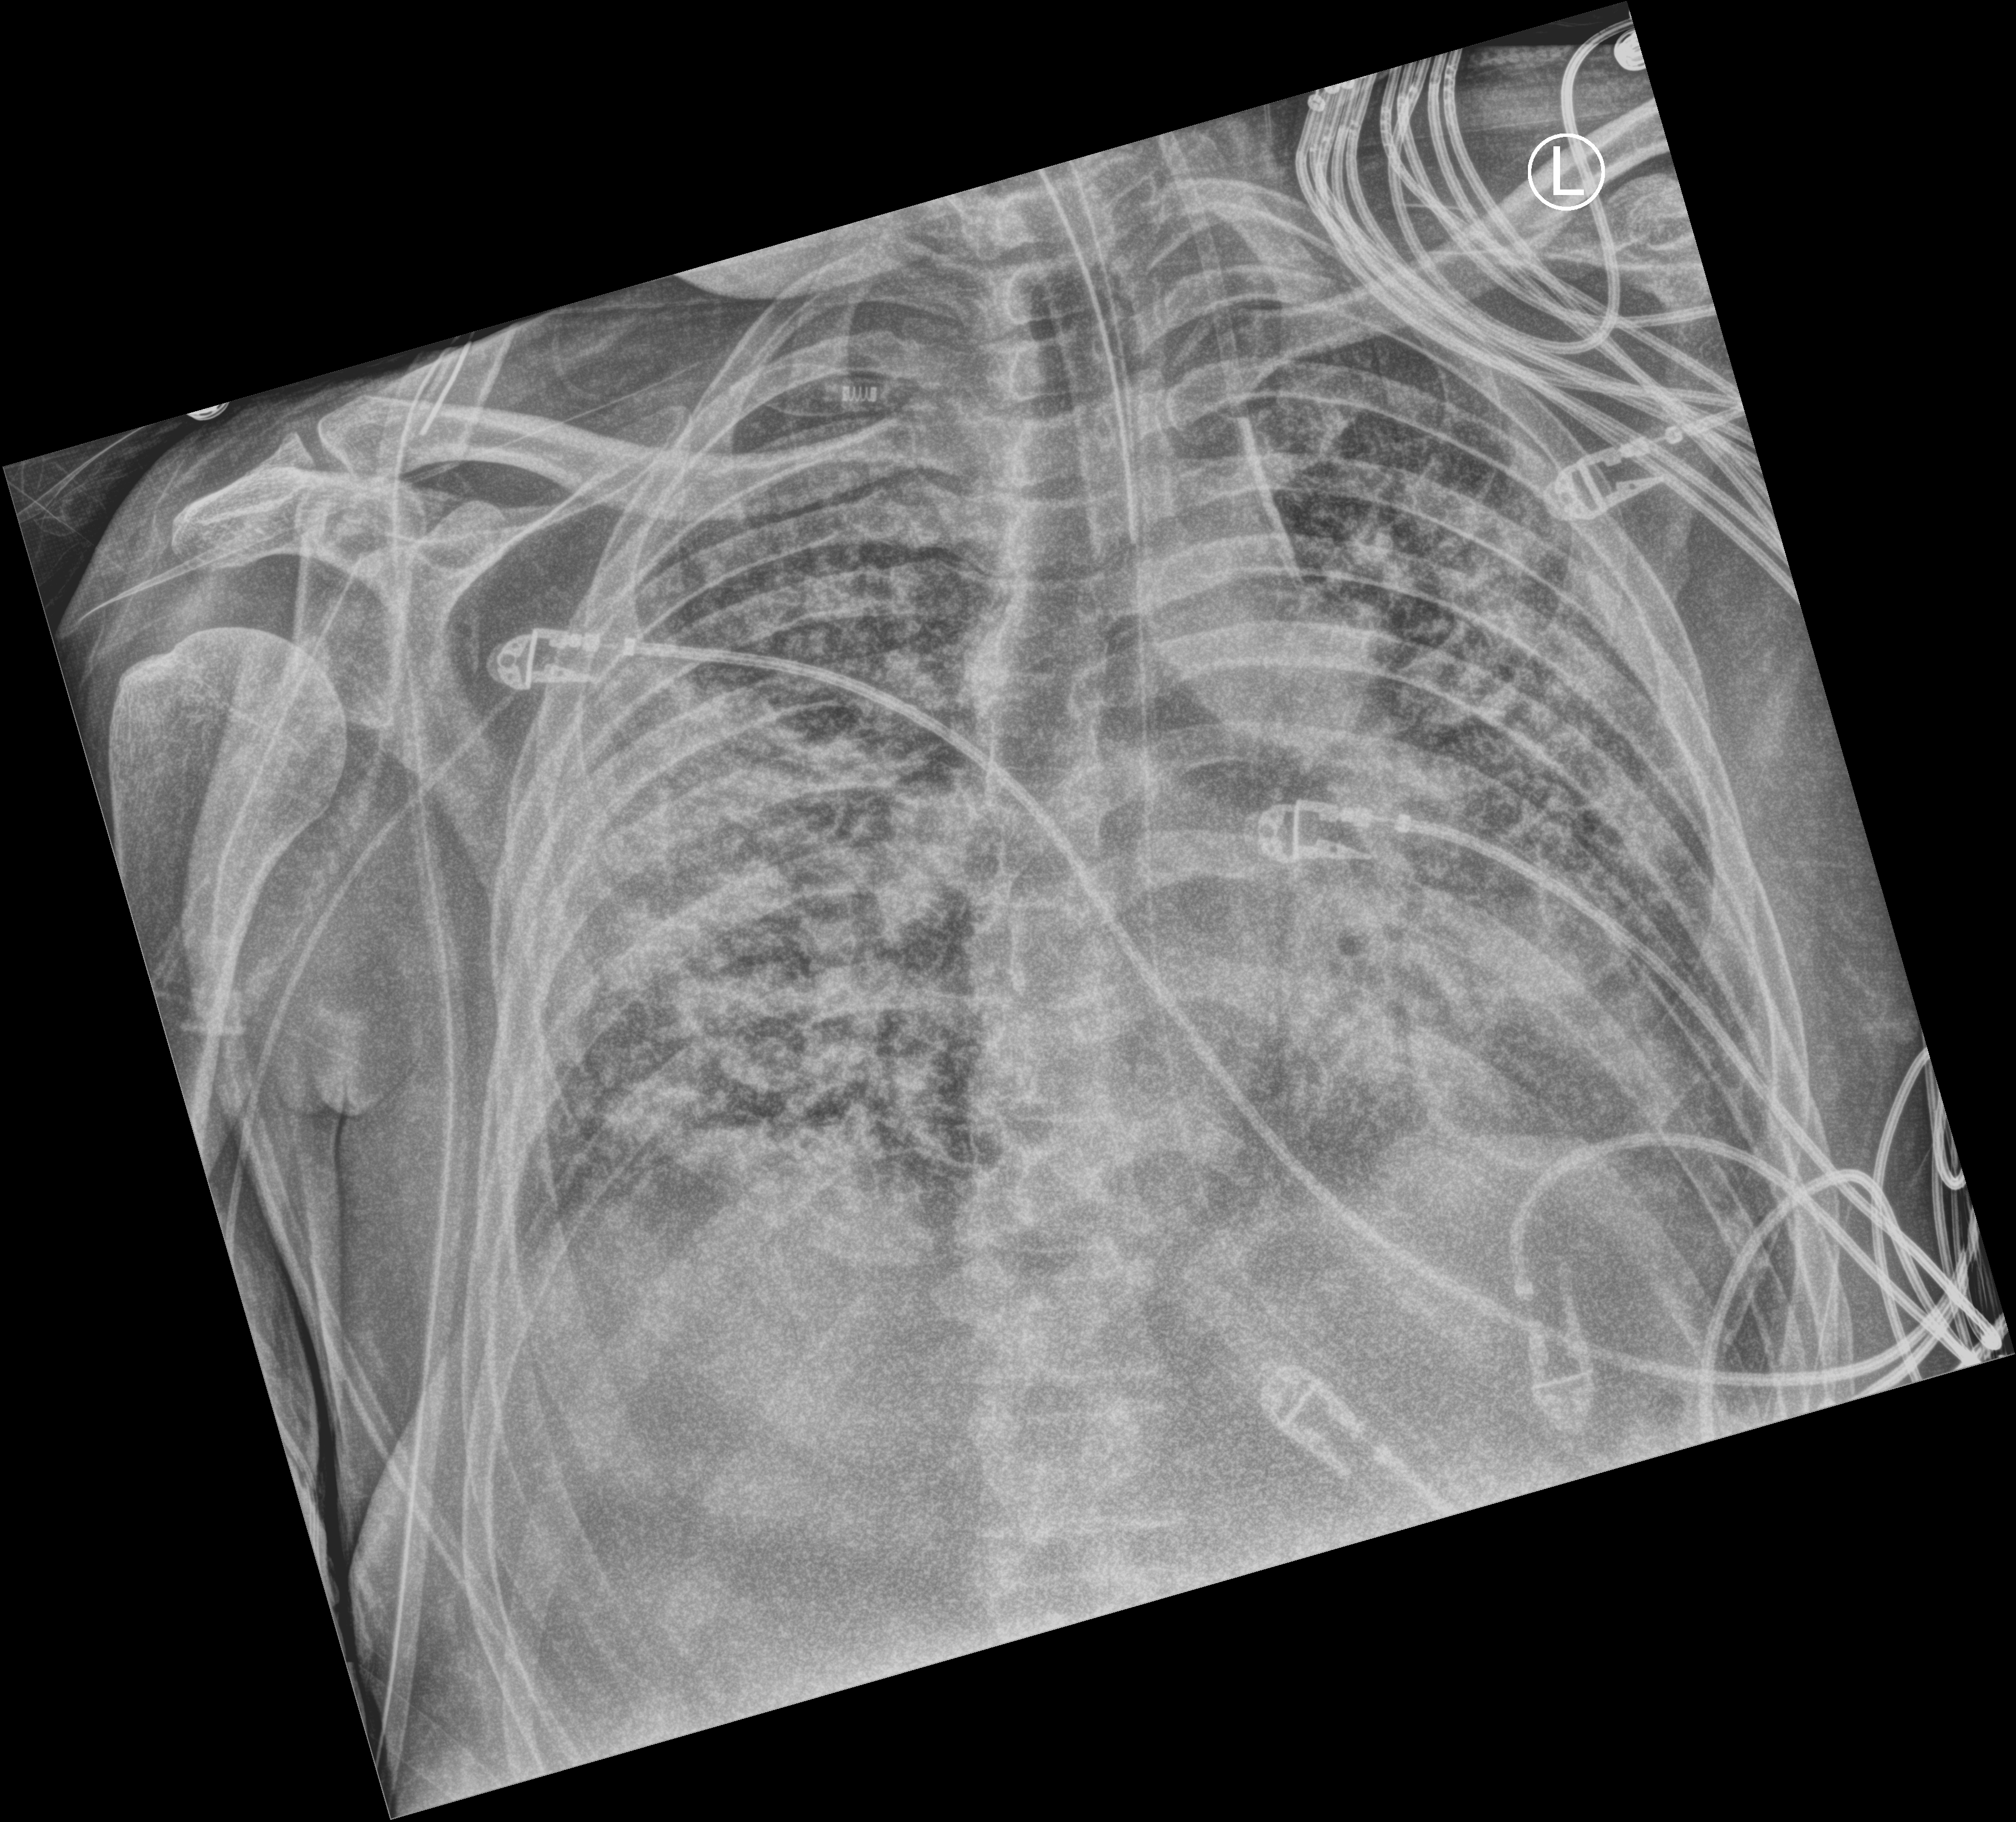
Chest X-ray (portable), anteroposterior (AP) projection. Patient hospitalised with COVID-19; male, aged 18–59 years.
Hospital-stay facts (about this admission, not read from this image; timing relative to this image not recorded): mechanically ventilated during this hospital stay: yes.